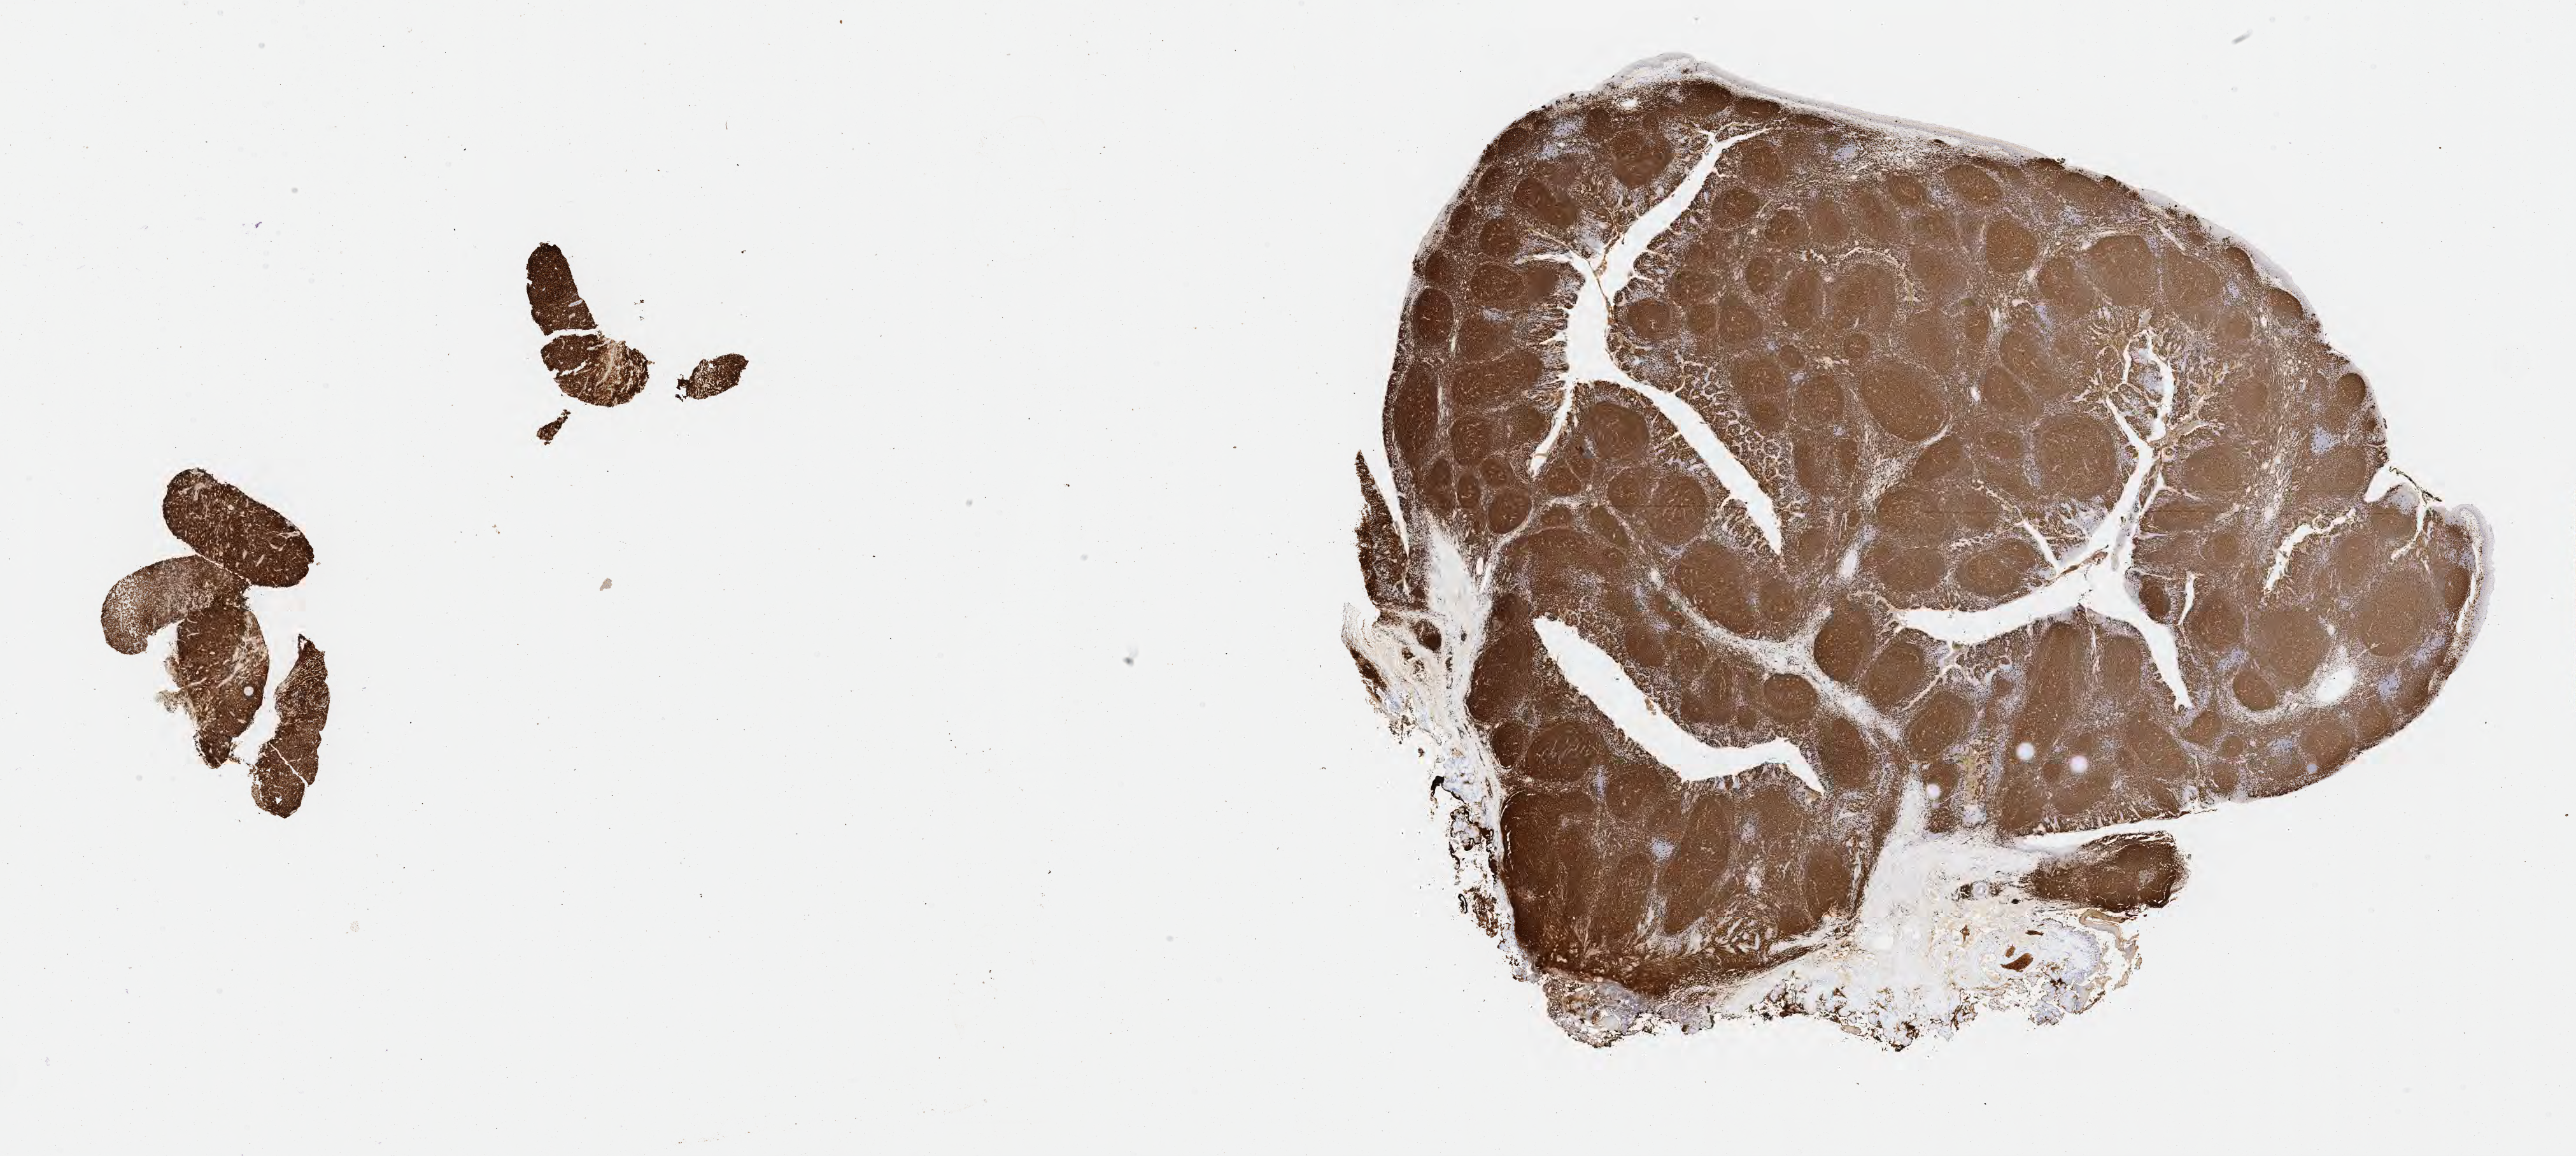
IHC for CD20, whole-slide image, low-resolution overview of the scanned area, about 32.7 x 14.7 mm, tumor tissue, site: lymph node. Male patient, age 54 years.
Diagnosis: Diffuse large B-cell lymphoma, NOS.